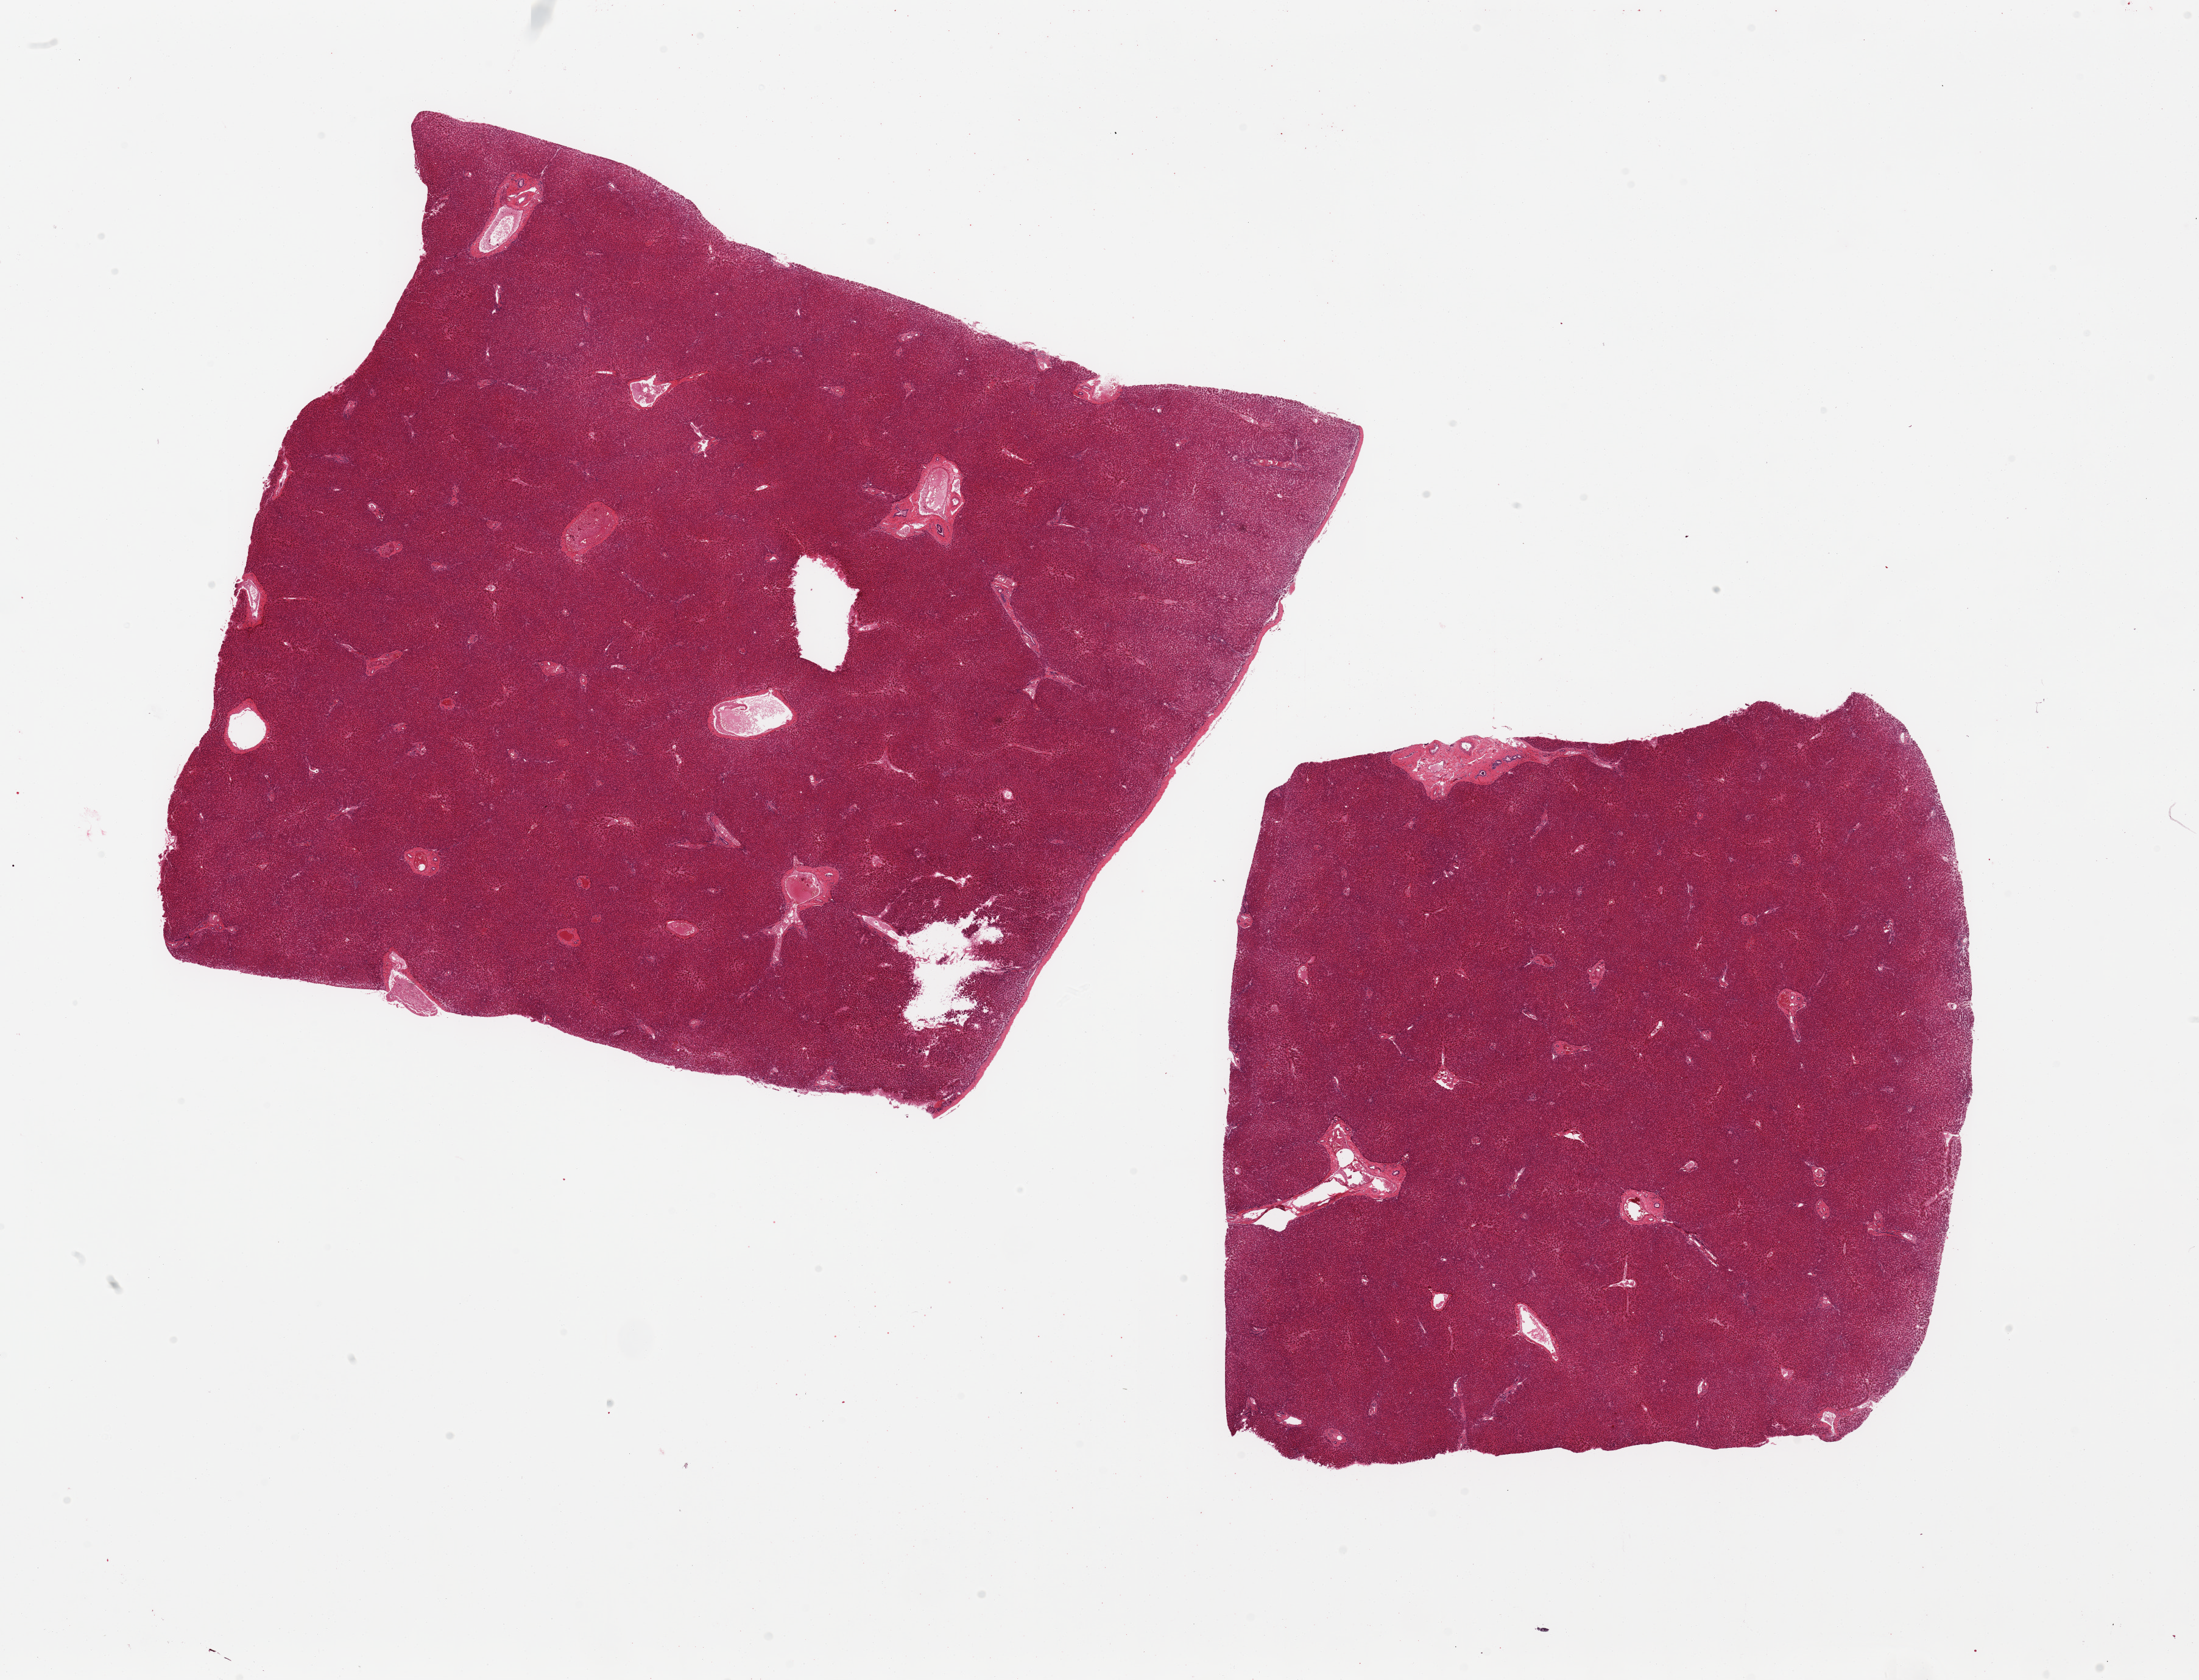
Digitized haematoxylin and eosin-stained section, brightfield, a low-resolution overview of the entire scanned area, about 28.5 x 21.8 mm (acquisition: 20x scan); PAXgene-fixed paraffin-embedded (PFPE) section; target tissue: liver; donor tissue sample. Male donor.
Pathologist's review note for this sample: 2 pieces; 1 piece includes capsule (target is 1 cm below capsule).